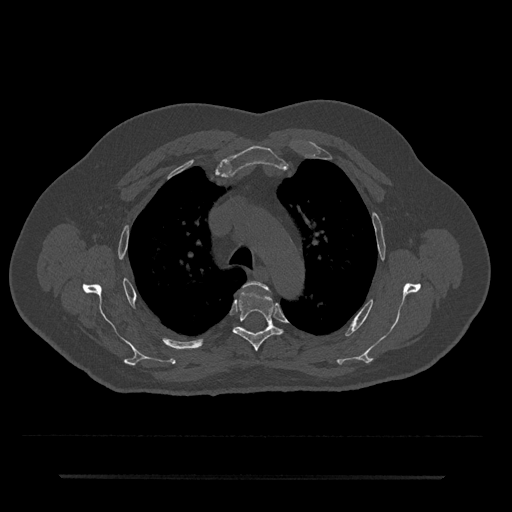
CT including the spine, one axial slice; position 528 of 797 along the scan axis; reconstruction kernel Br40s/3; 120 kVp; bone window (W 1800 / L 400 HU); 0.5 mm slice thickness; 512 × 512 image matrix, field of view 437 × 437 mm. Patient: male, 69 years. From the clinical record (not read from this slice): primary cancer: prostate.
Annotated regions visible in this slice (semi-automatically segmented with operator editing):
- T3 vertebra: box from (x=244, y=281) to (x=268, y=290) px
- T4 vertebra: (x=233, y=291)–(x=283, y=351)